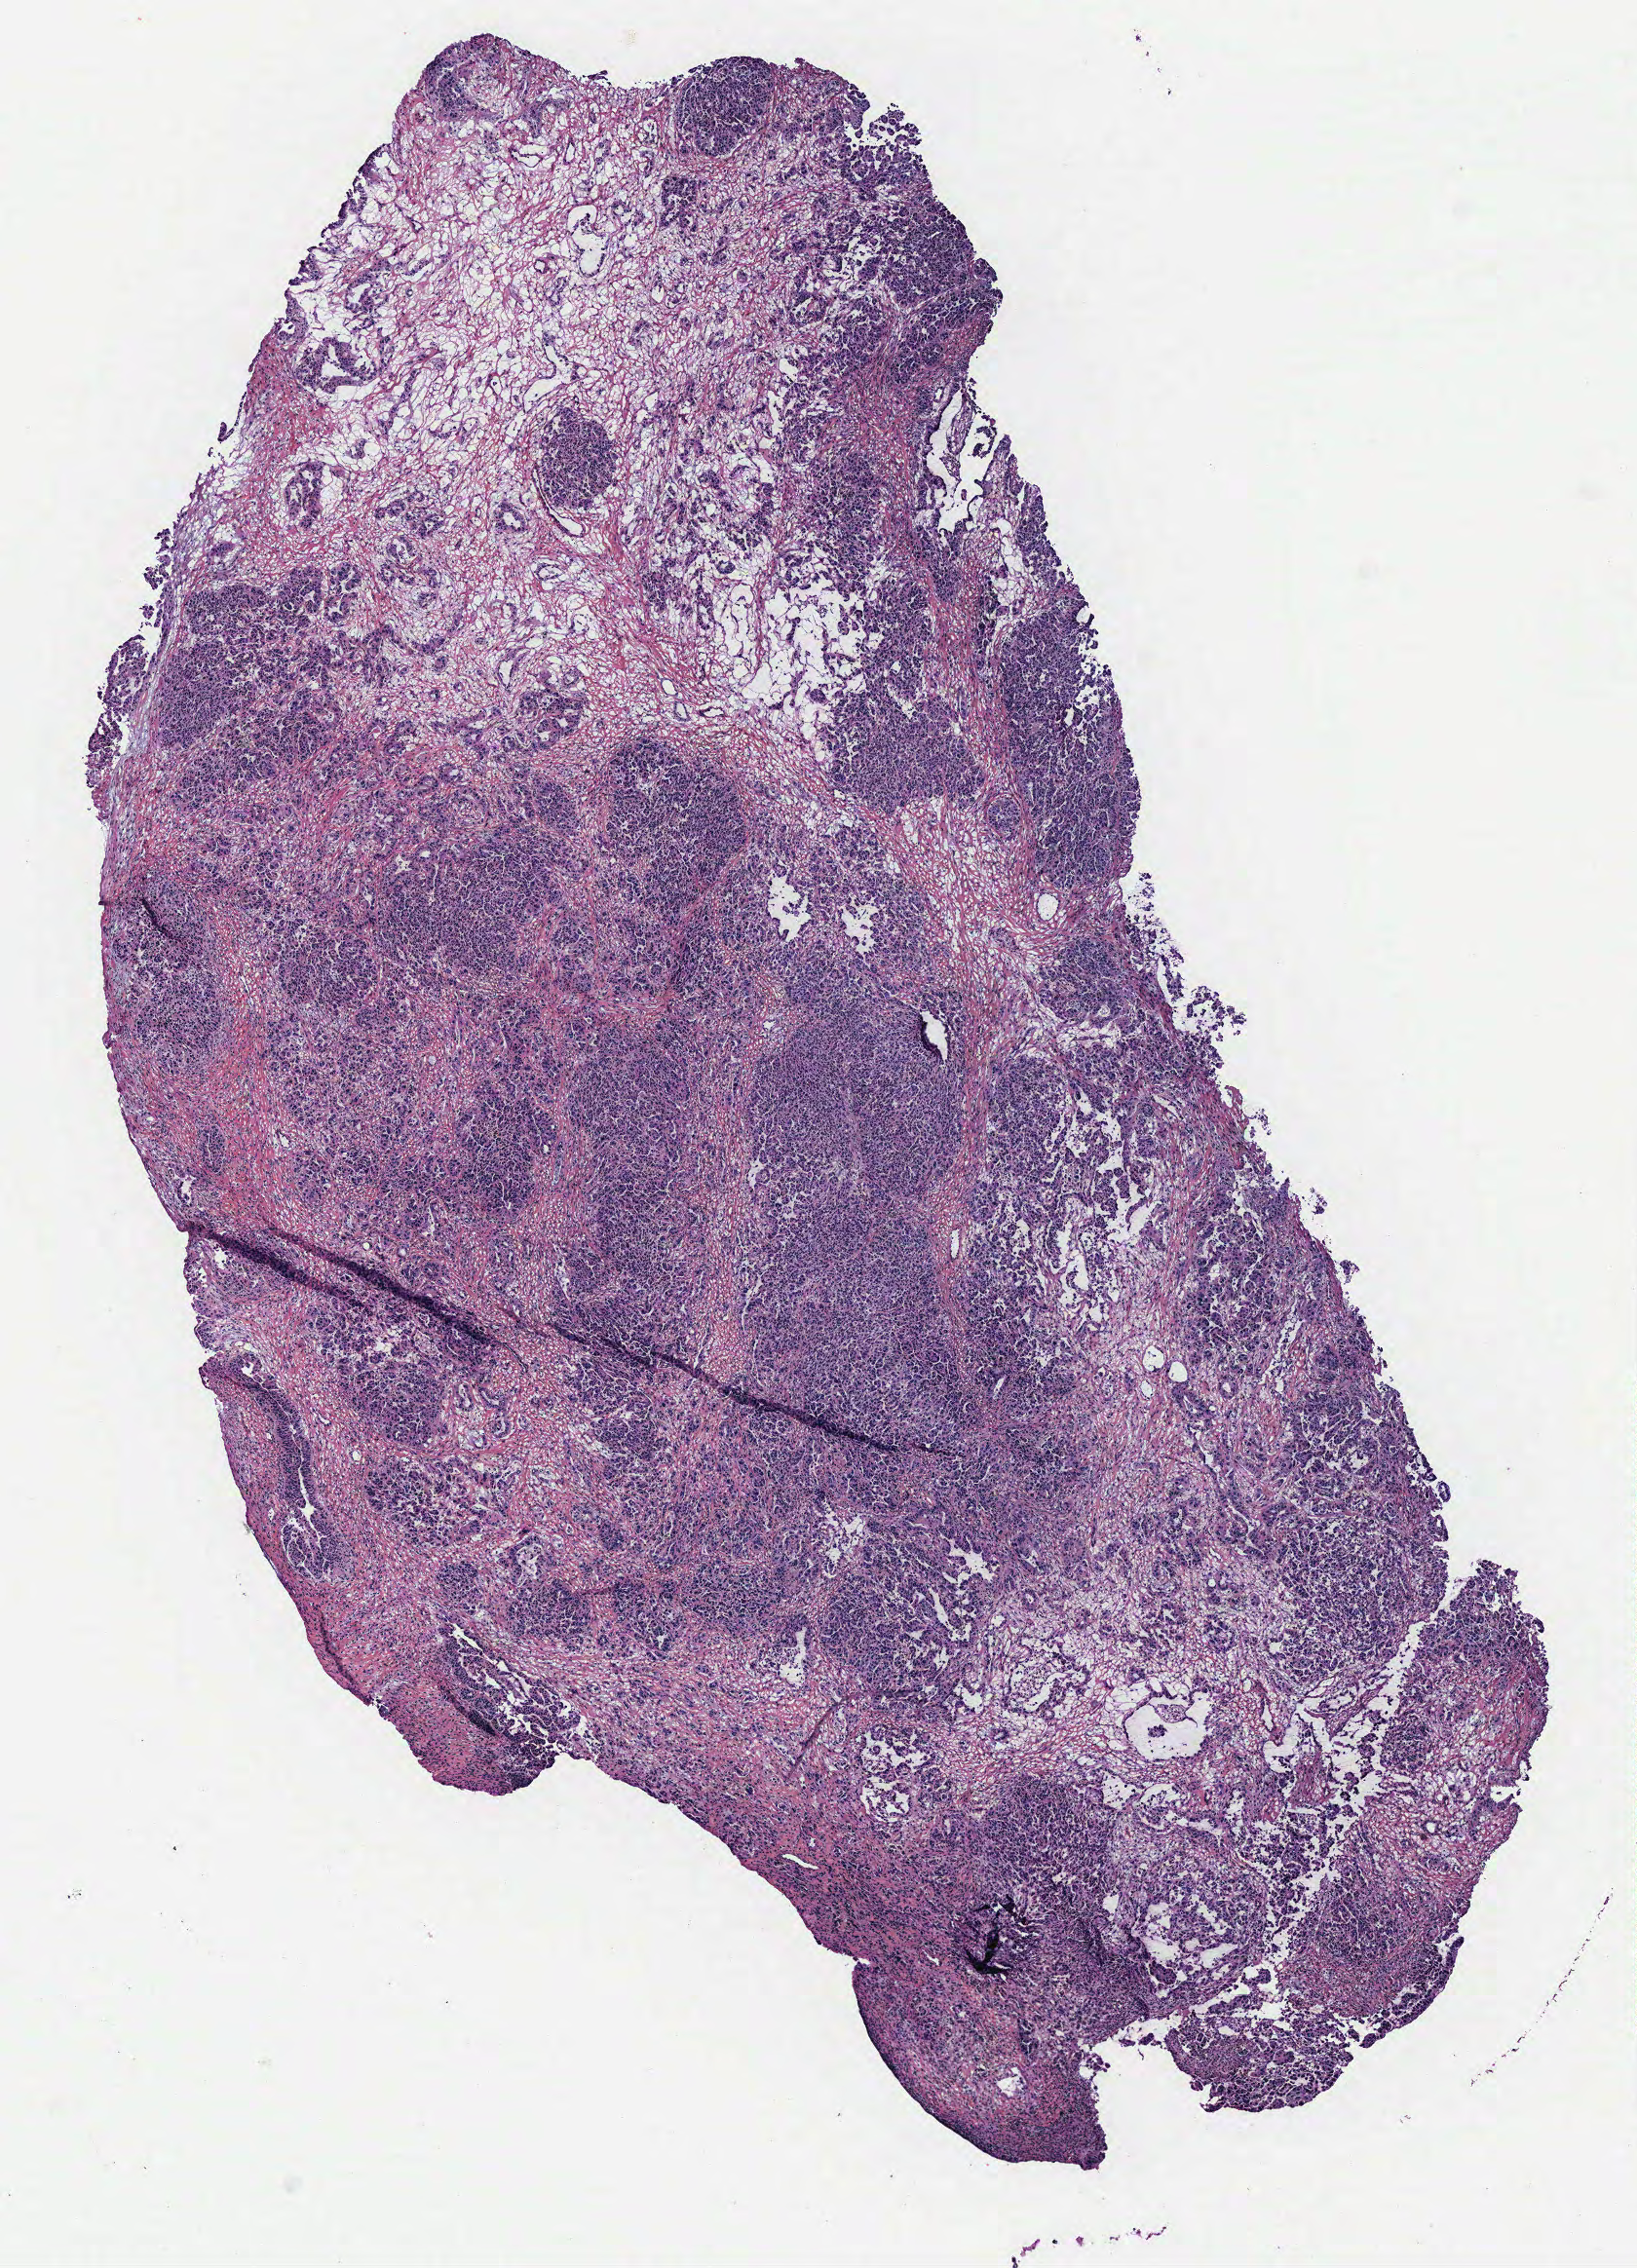
Whole-slide histology image, H&E-stained, a low-resolution overview of the entire scanned area, about 6.7 x 9.3 mm; tumour tissue sample, ovary. Patient: female, age 58 years.
Primary tumour site (as recorded): ovary. Diagnosis: Serous adenocarcinoma, NOS.